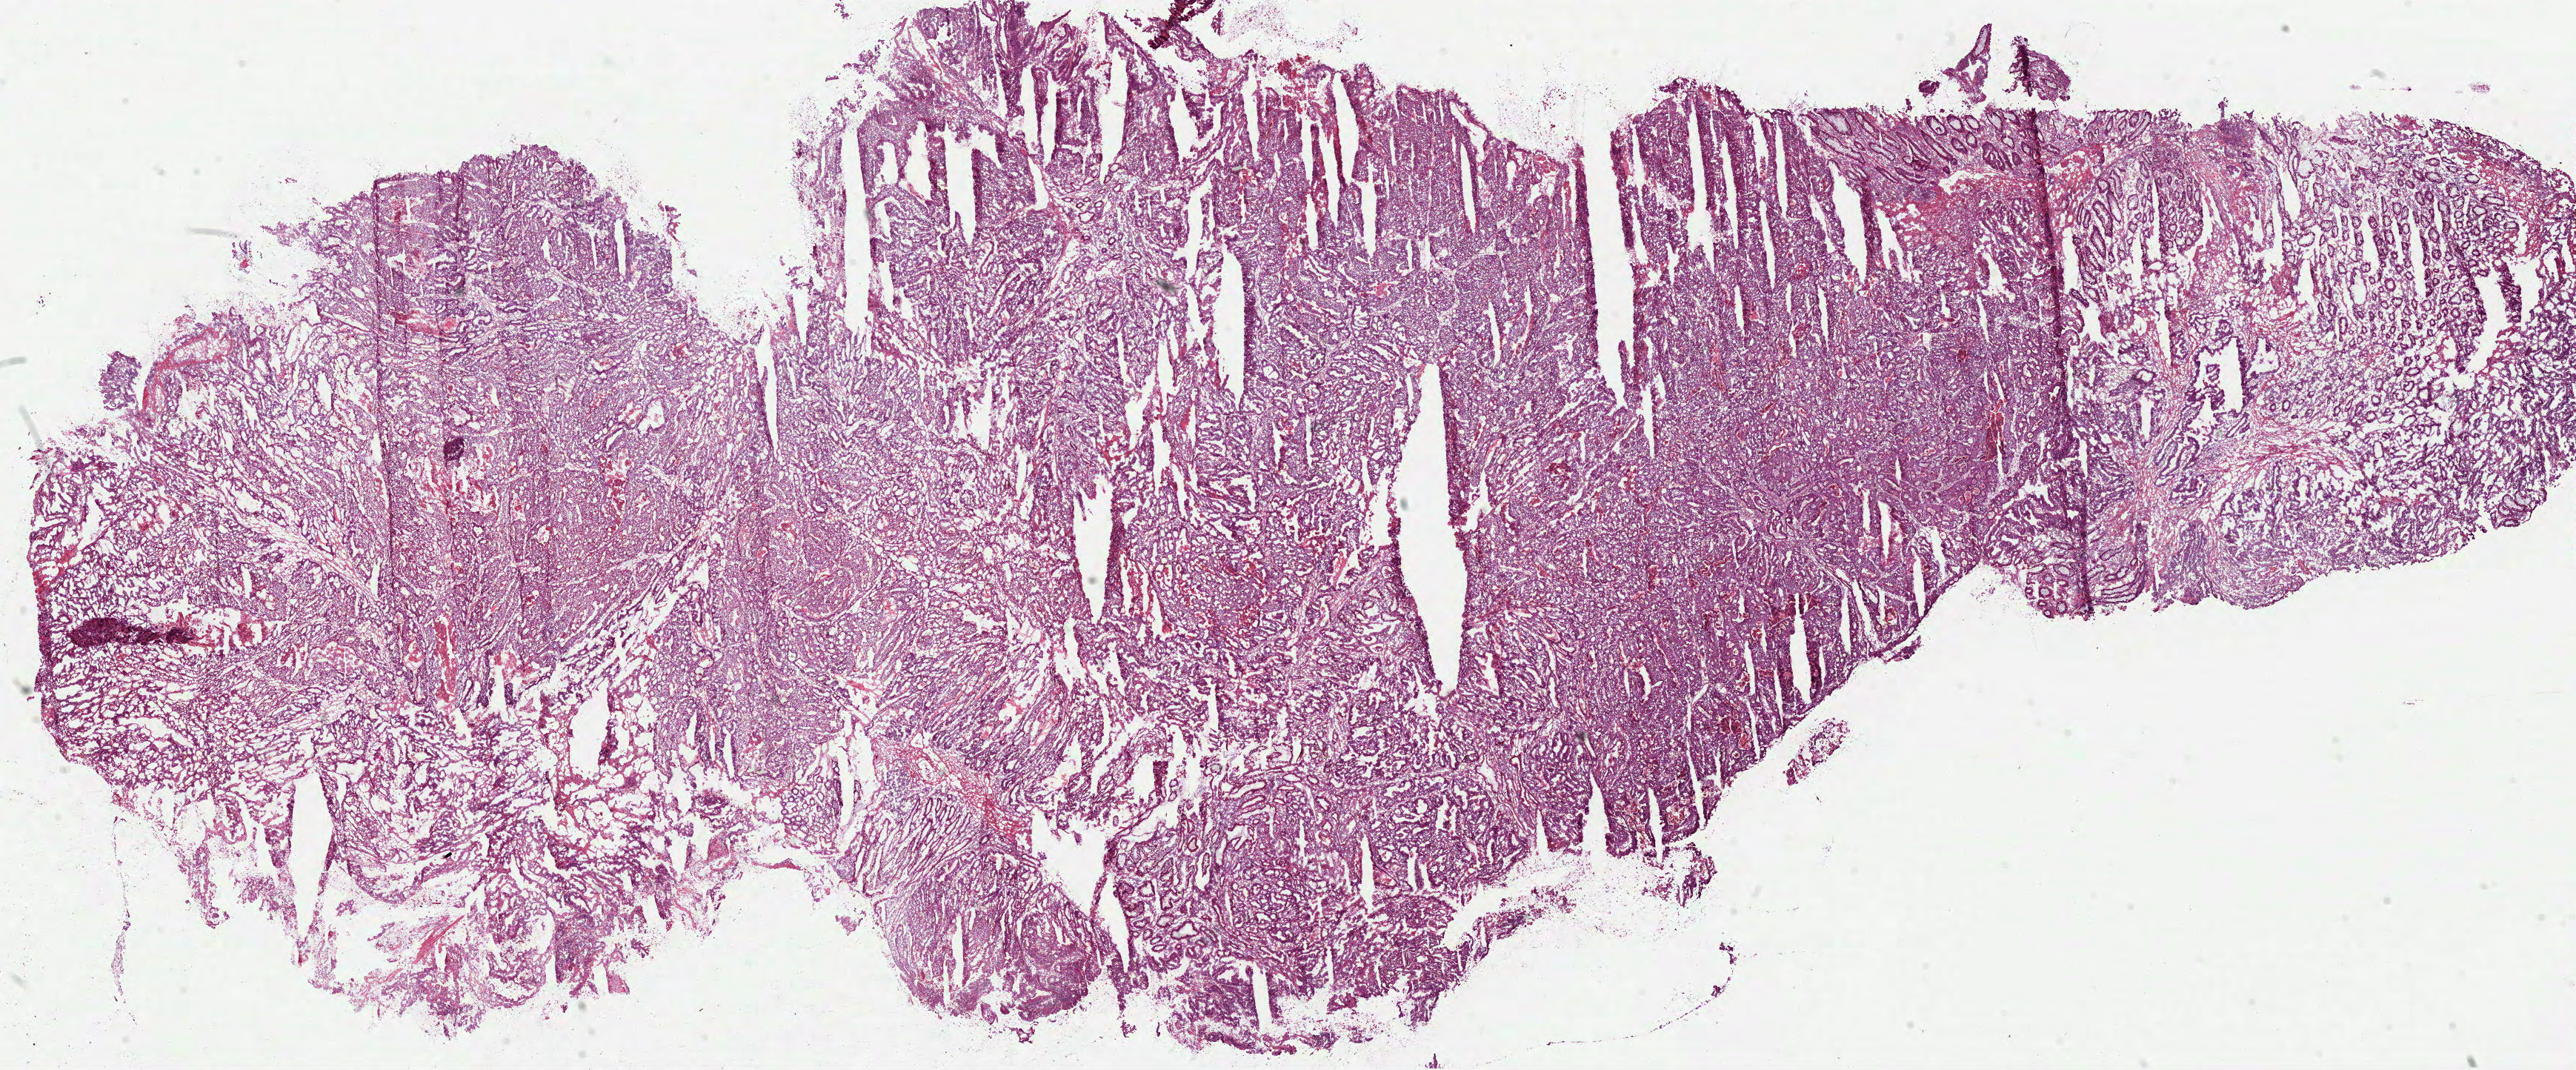
H&E-stained whole-slide image — low-resolution overview of the scanned area, about 28.0 x 11.6 mm (from a 40x scan), frozen section from the top of the tissue portion, colon, primary tumour sample. Male patient; age at initial diagnosis 81 years. Slide review estimates, as recorded: tumour cells 62%, tumour nuclei 80%, normal cells 18%, stromal cells 10%, necrosis 10%.
Lymph nodes positive (case pathology): 10 of 17 examined. AJCC pathologic stage: IV (6th edition). TNM: T4 N2 M1. Histologic diagnosis: Adenocarcinoma, NOS (cecum).